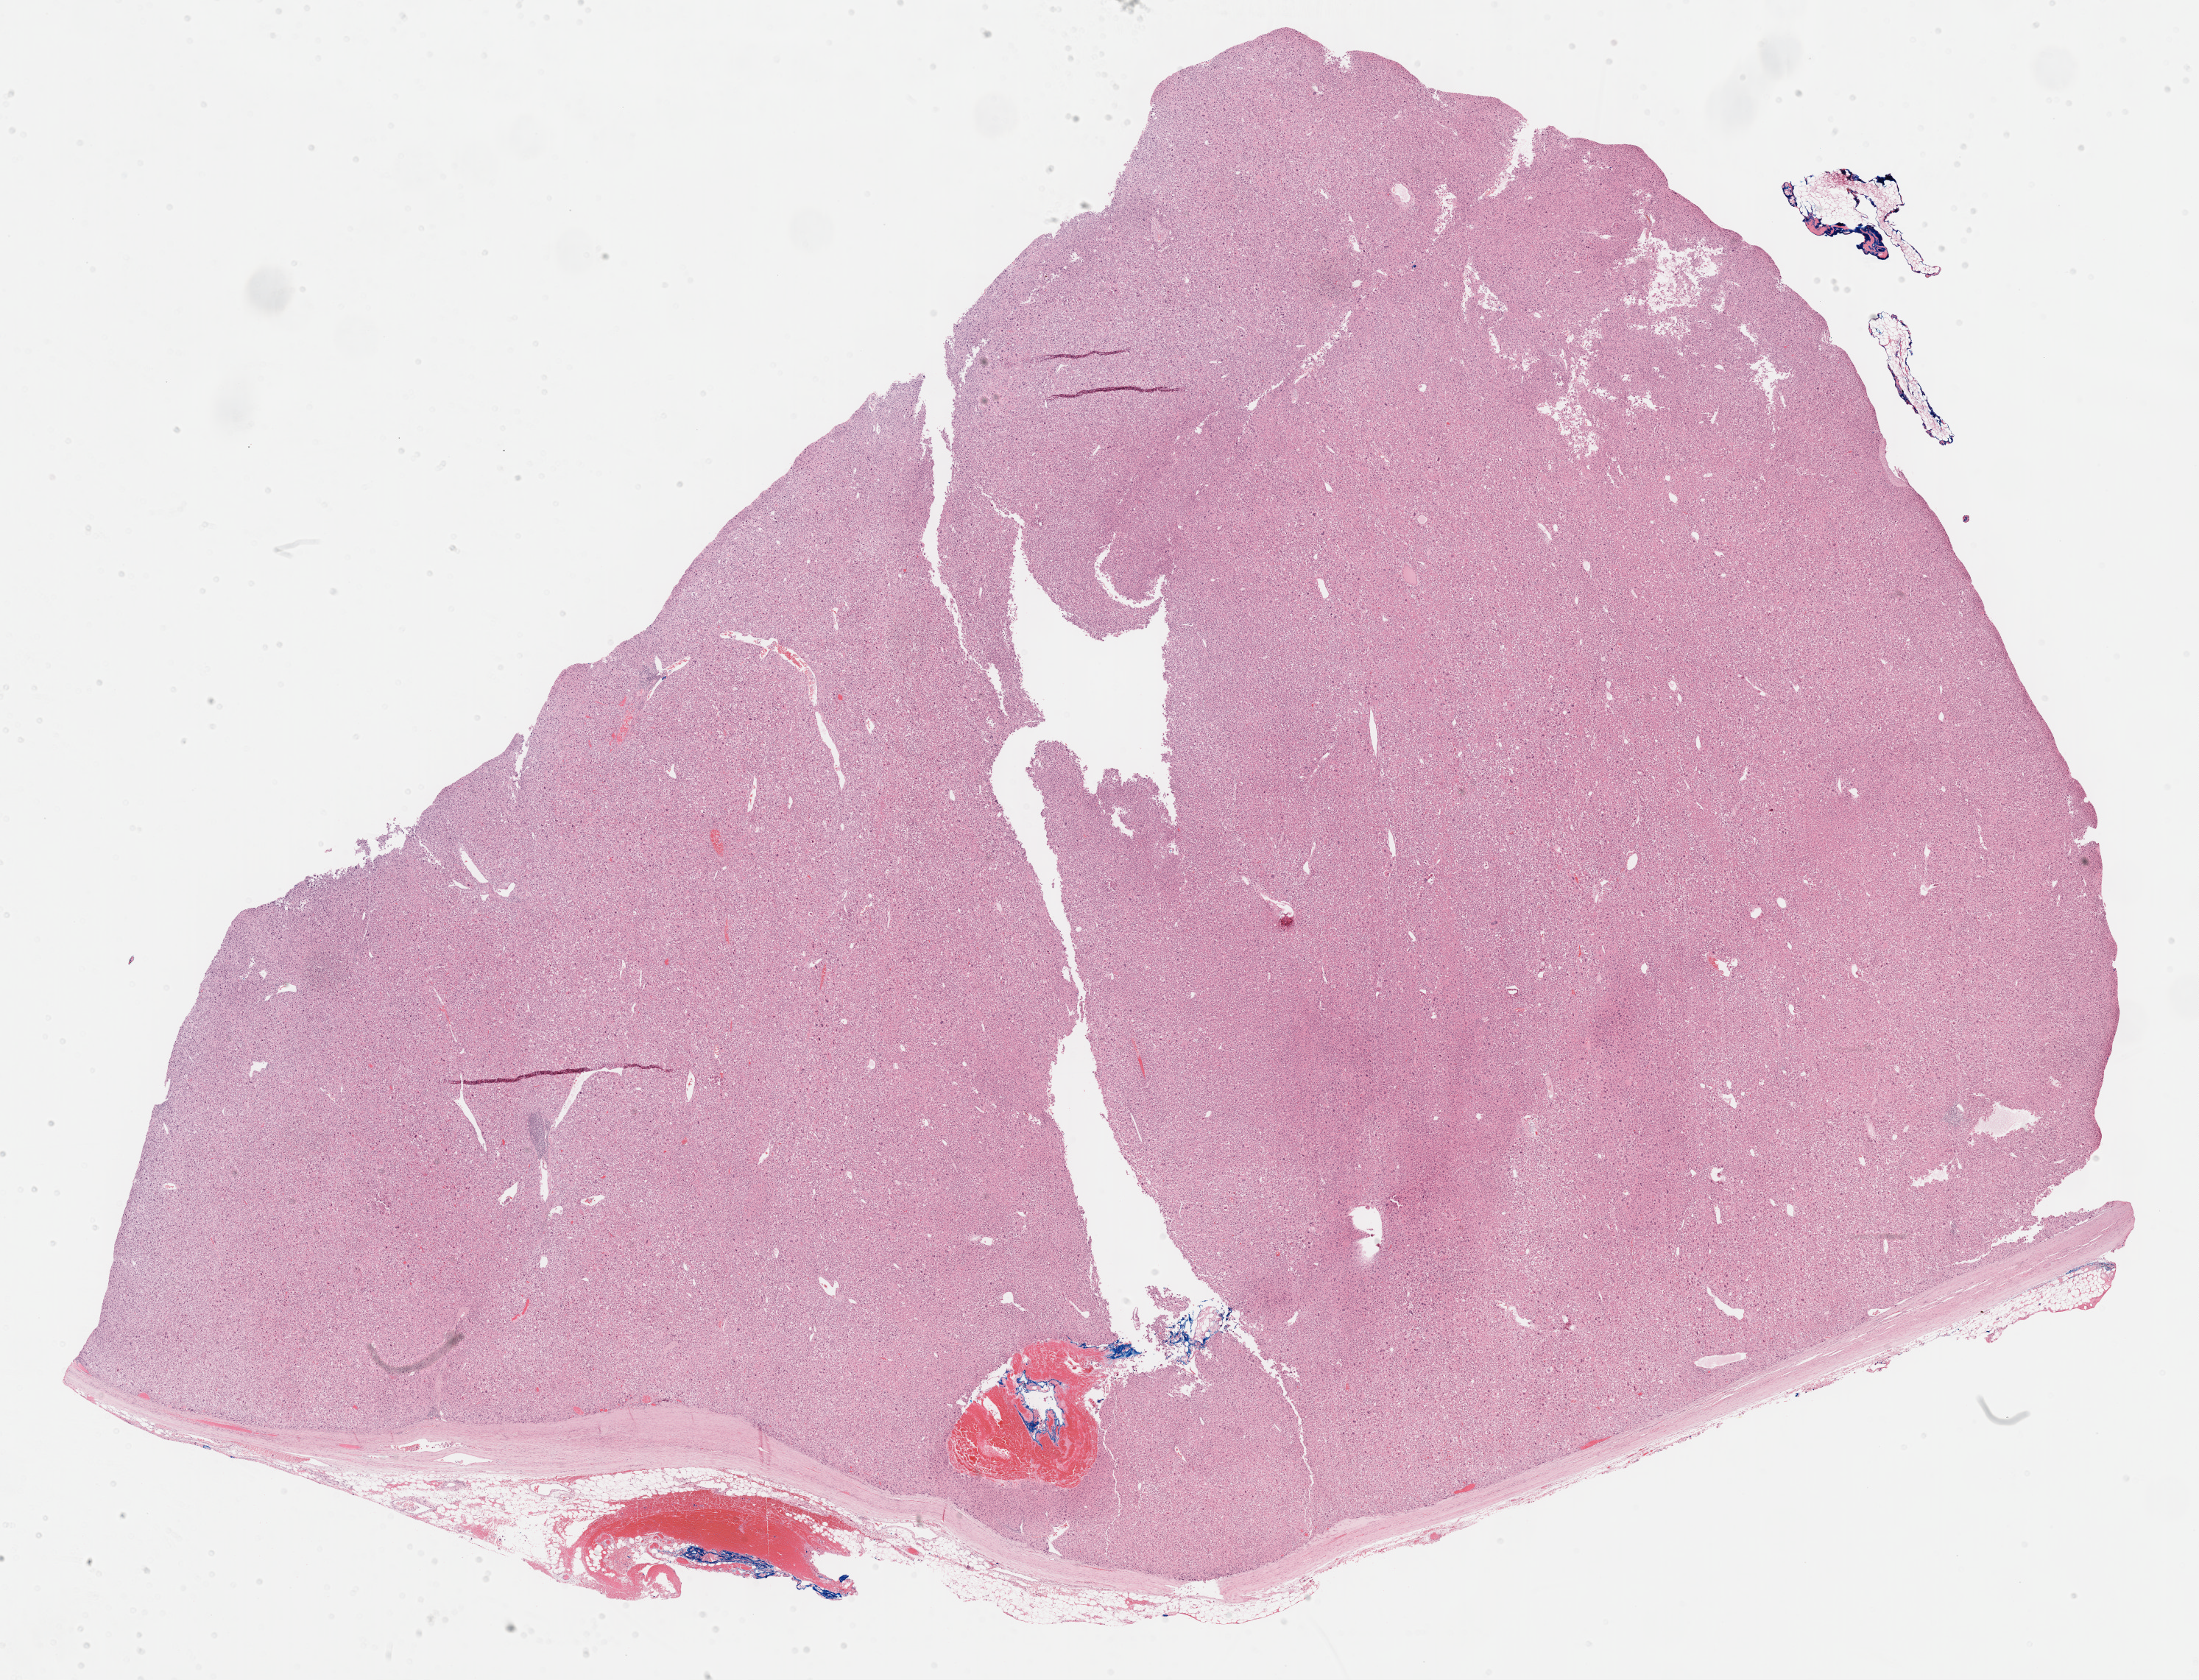
H&E-stained whole-slide image — whole scanned area (about 24.2 x 18.5 mm, acquisition: 40x scan) shown as a low-resolution overview. FFPE section. Sample: primary tumour, adrenal cortex. Patient: female, age at initial diagnosis 64 years.
Laterality: right. Pathologic diagnosis: Adrenal cortical carcinoma (cortex of adrenal gland).